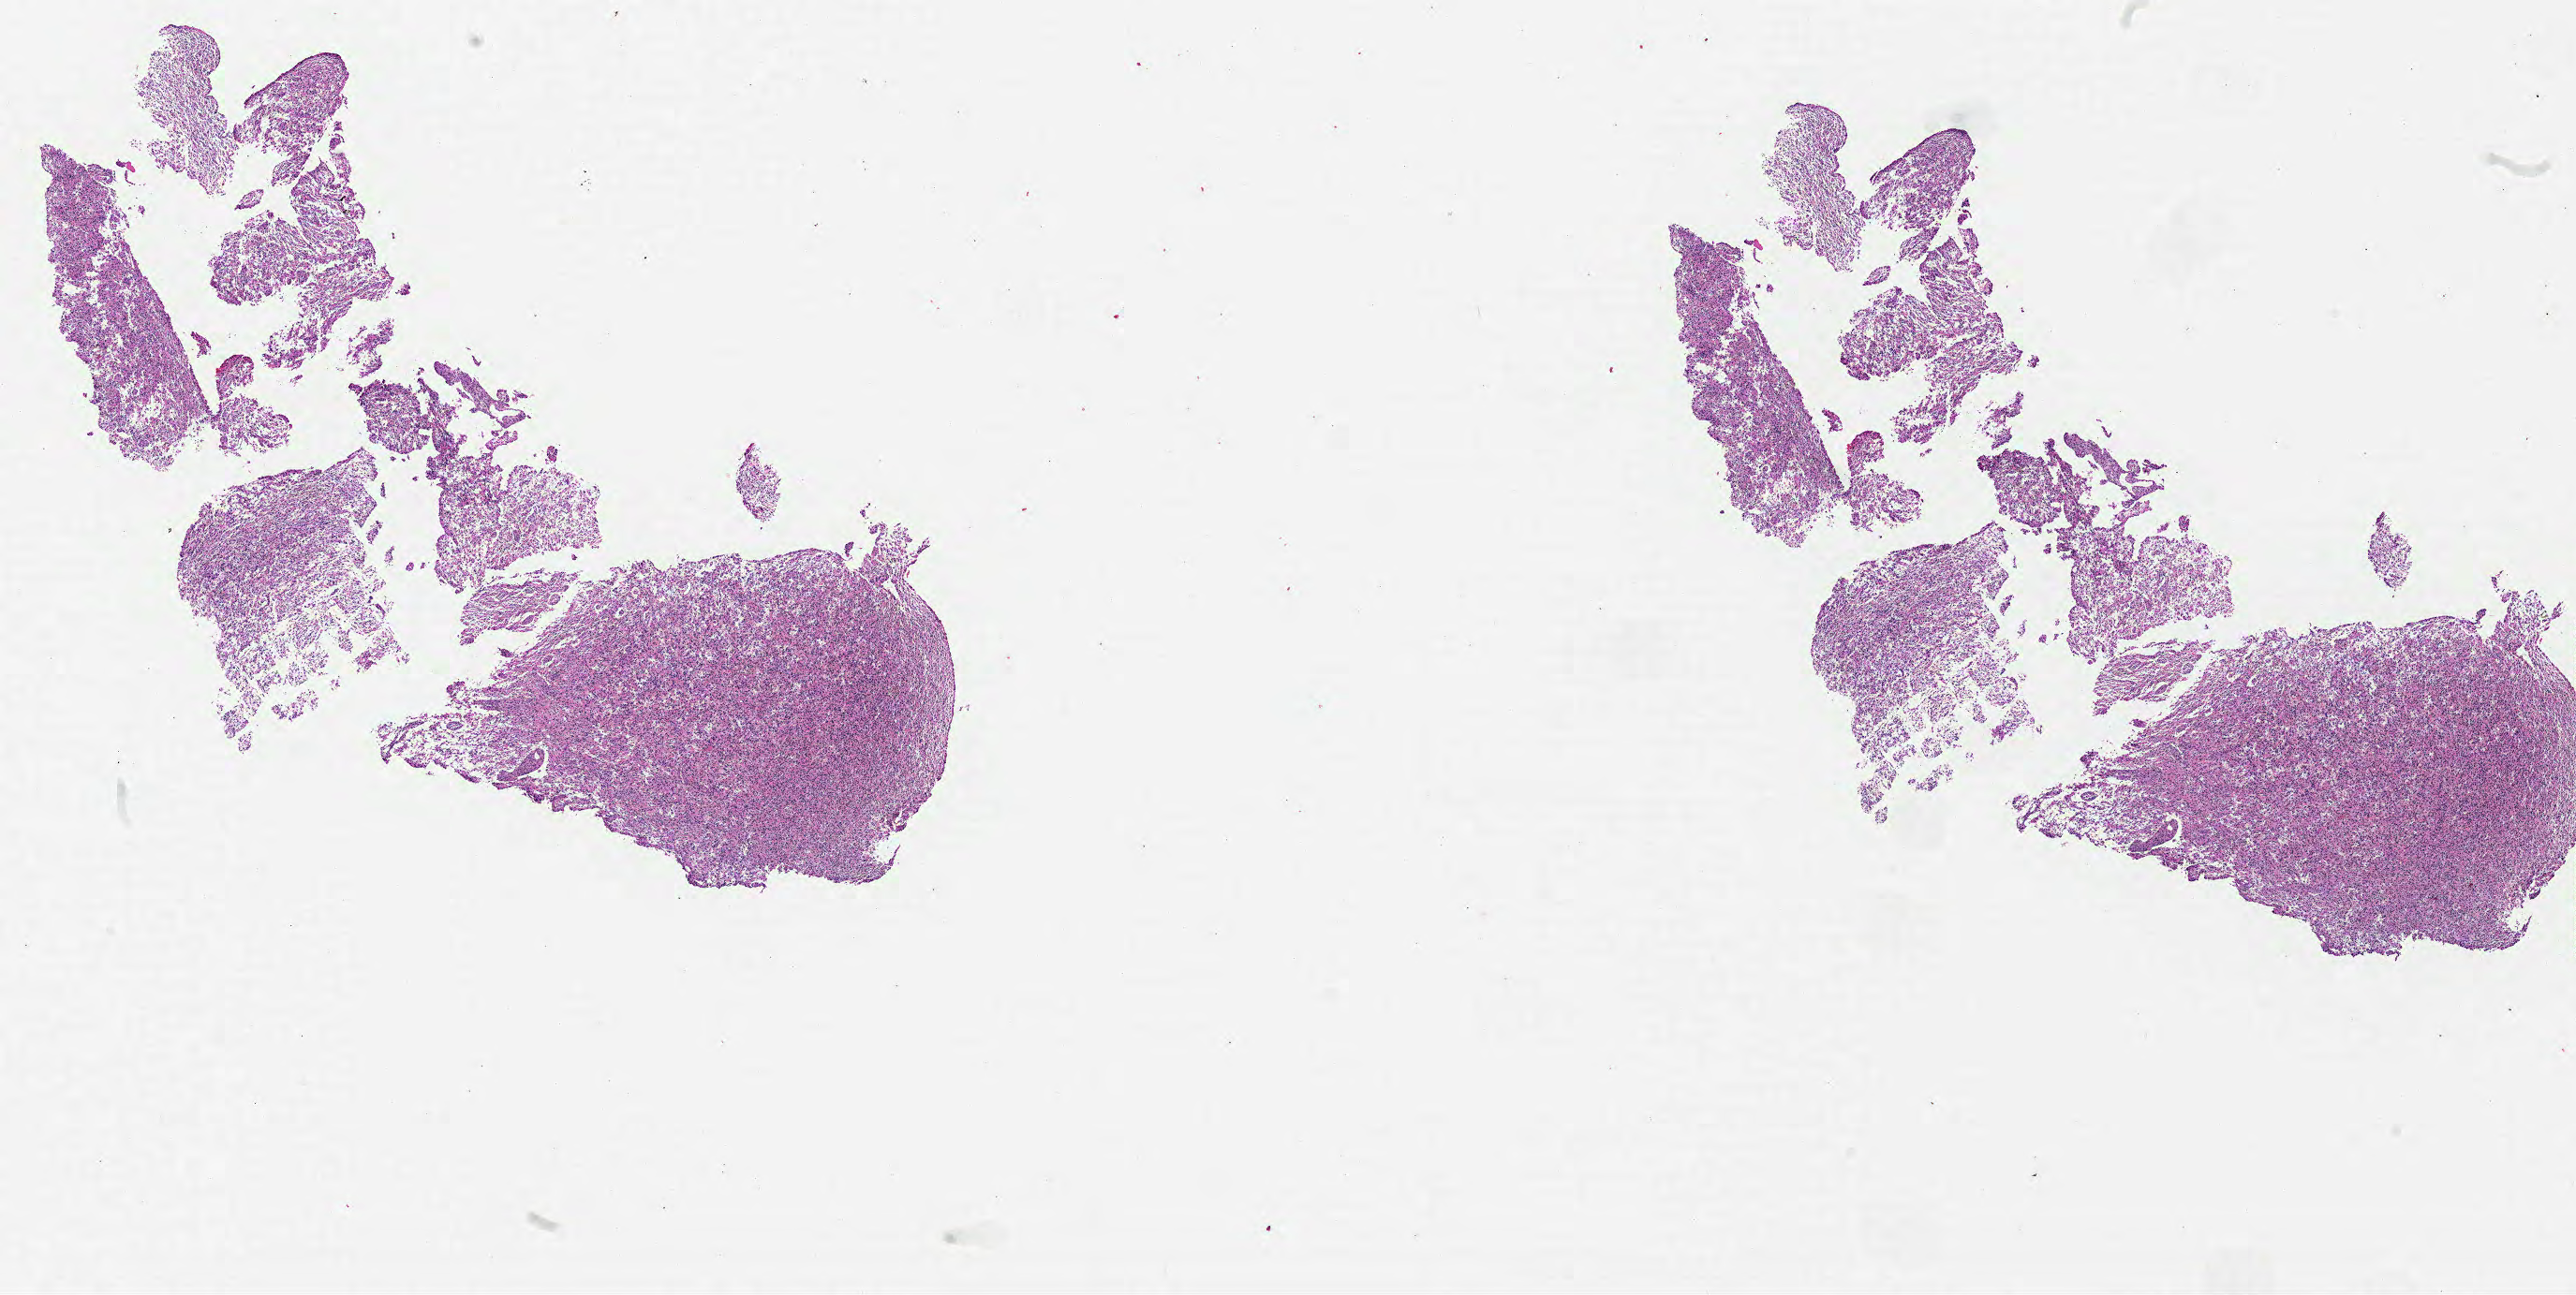
Whole-slide histology image, H&E, shown as a low-resolution overview of the whole scanned area (about 22.0 x 11.1 mm, acquisition: 20x scan); FFPE section; sample: primary tumour, brain. Female patient; age at initial diagnosis 75 years.
Pathologic diagnosis: Glioblastoma.